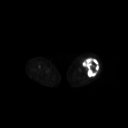
FDG PET of an extremity soft-tissue mass (from a PET/CT study), one axial slice; 128 × 128 image matrix. Female patient, age 62 years. From the clinical record (not read from this slice): histological type: undifferentiated – high grade; grade: high; site of the primary tumour: left thigh.
Structures marked on this image (expert contour drawn on MRI and transferred to this co-registered scan by the dataset authors):
- gross tumour volume including surrounding oedema: bounding box (x1, y1, x2, y2) in pixels: (82, 58, 99, 77)
- gross tumour volume (mass): (83, 58, 99, 77)